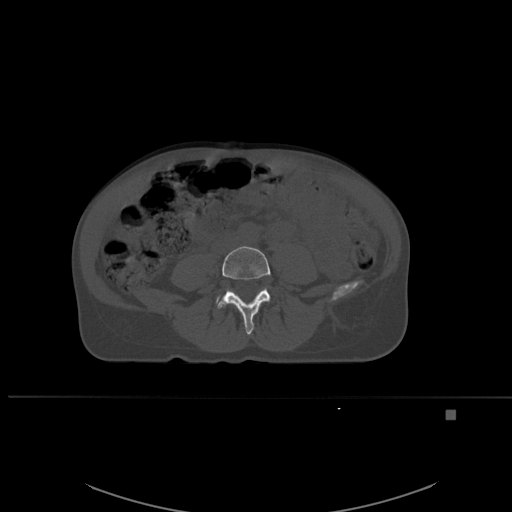
CT including the spine, one axial slice. Slice 189 of 537 in the series (ordered by position). Bone window (W 1800 / L 400 HU). 1.5 mm slice thickness. 512 × 512 image matrix, field of view 440 × 440 mm. Female patient, age 45 years. Case-level facts recorded for this patient, not image findings: primary cancer: lung.
Annotated regions visible in this slice (semi-automatically segmented with operator editing):
- L4 vertebra: box from (x=216, y=246) to (x=271, y=335) px
- L5 vertebra: (x=216, y=297)–(x=218, y=301)